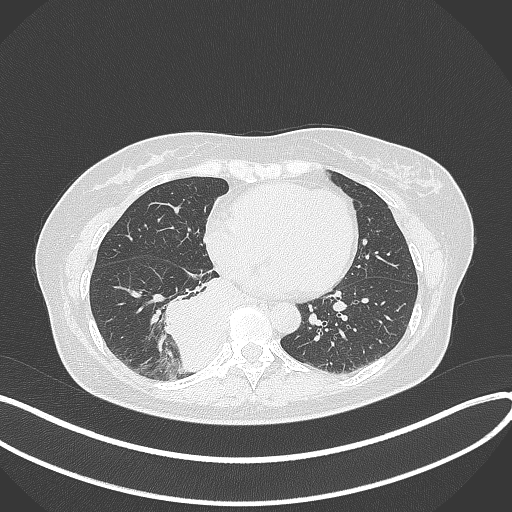
Chest CT, one axial slice; position 133 of 331 along the scan axis; reconstruction kernel B70f; 120 kVp; lung window (W 1500 / L -600 HU); 1 mm slice thickness; 512 × 512 image matrix, field of view 400 × 400 mm. Female patient, age 54 years. Case-level facts recorded for this patient, not image findings: clinical TNM (as recorded): T4 N0 M0.
Annotated regions visible in this slice (bounding box drawn by a radiologist):
- lung tumour (recorded histology: adenocarcinoma): bounding box <158,269,236,370> (left, top, right, bottom; pixels)